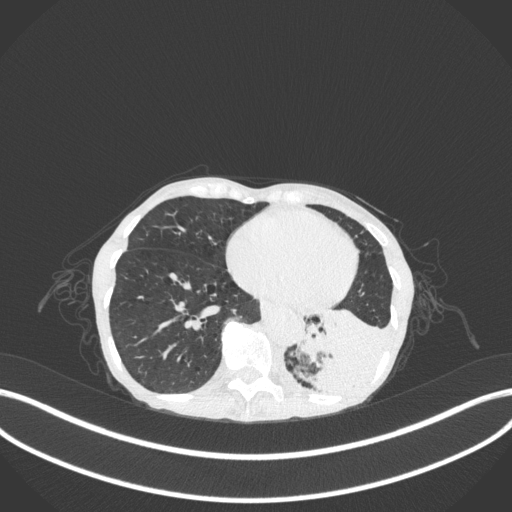
Chest CT, one axial slice. Slice 76 of 347 in the series (ordered by position). Reconstruction kernel B31f. Lung window (W 1500 / L -600 HU). 512 × 512 image matrix, field of view 400 × 400 mm. Female patient, age 70 years. Case-level facts recorded for this patient, not image findings: clinical TNM (as recorded): T3 N0 M0; histopathological grade: G3.
Annotated regions visible in this slice (bounding box drawn by a radiologist):
- lung tumour (recorded histology: small cell carcinoma): bounding box [x1, y1, x2, y2] px = [296, 298, 397, 403]